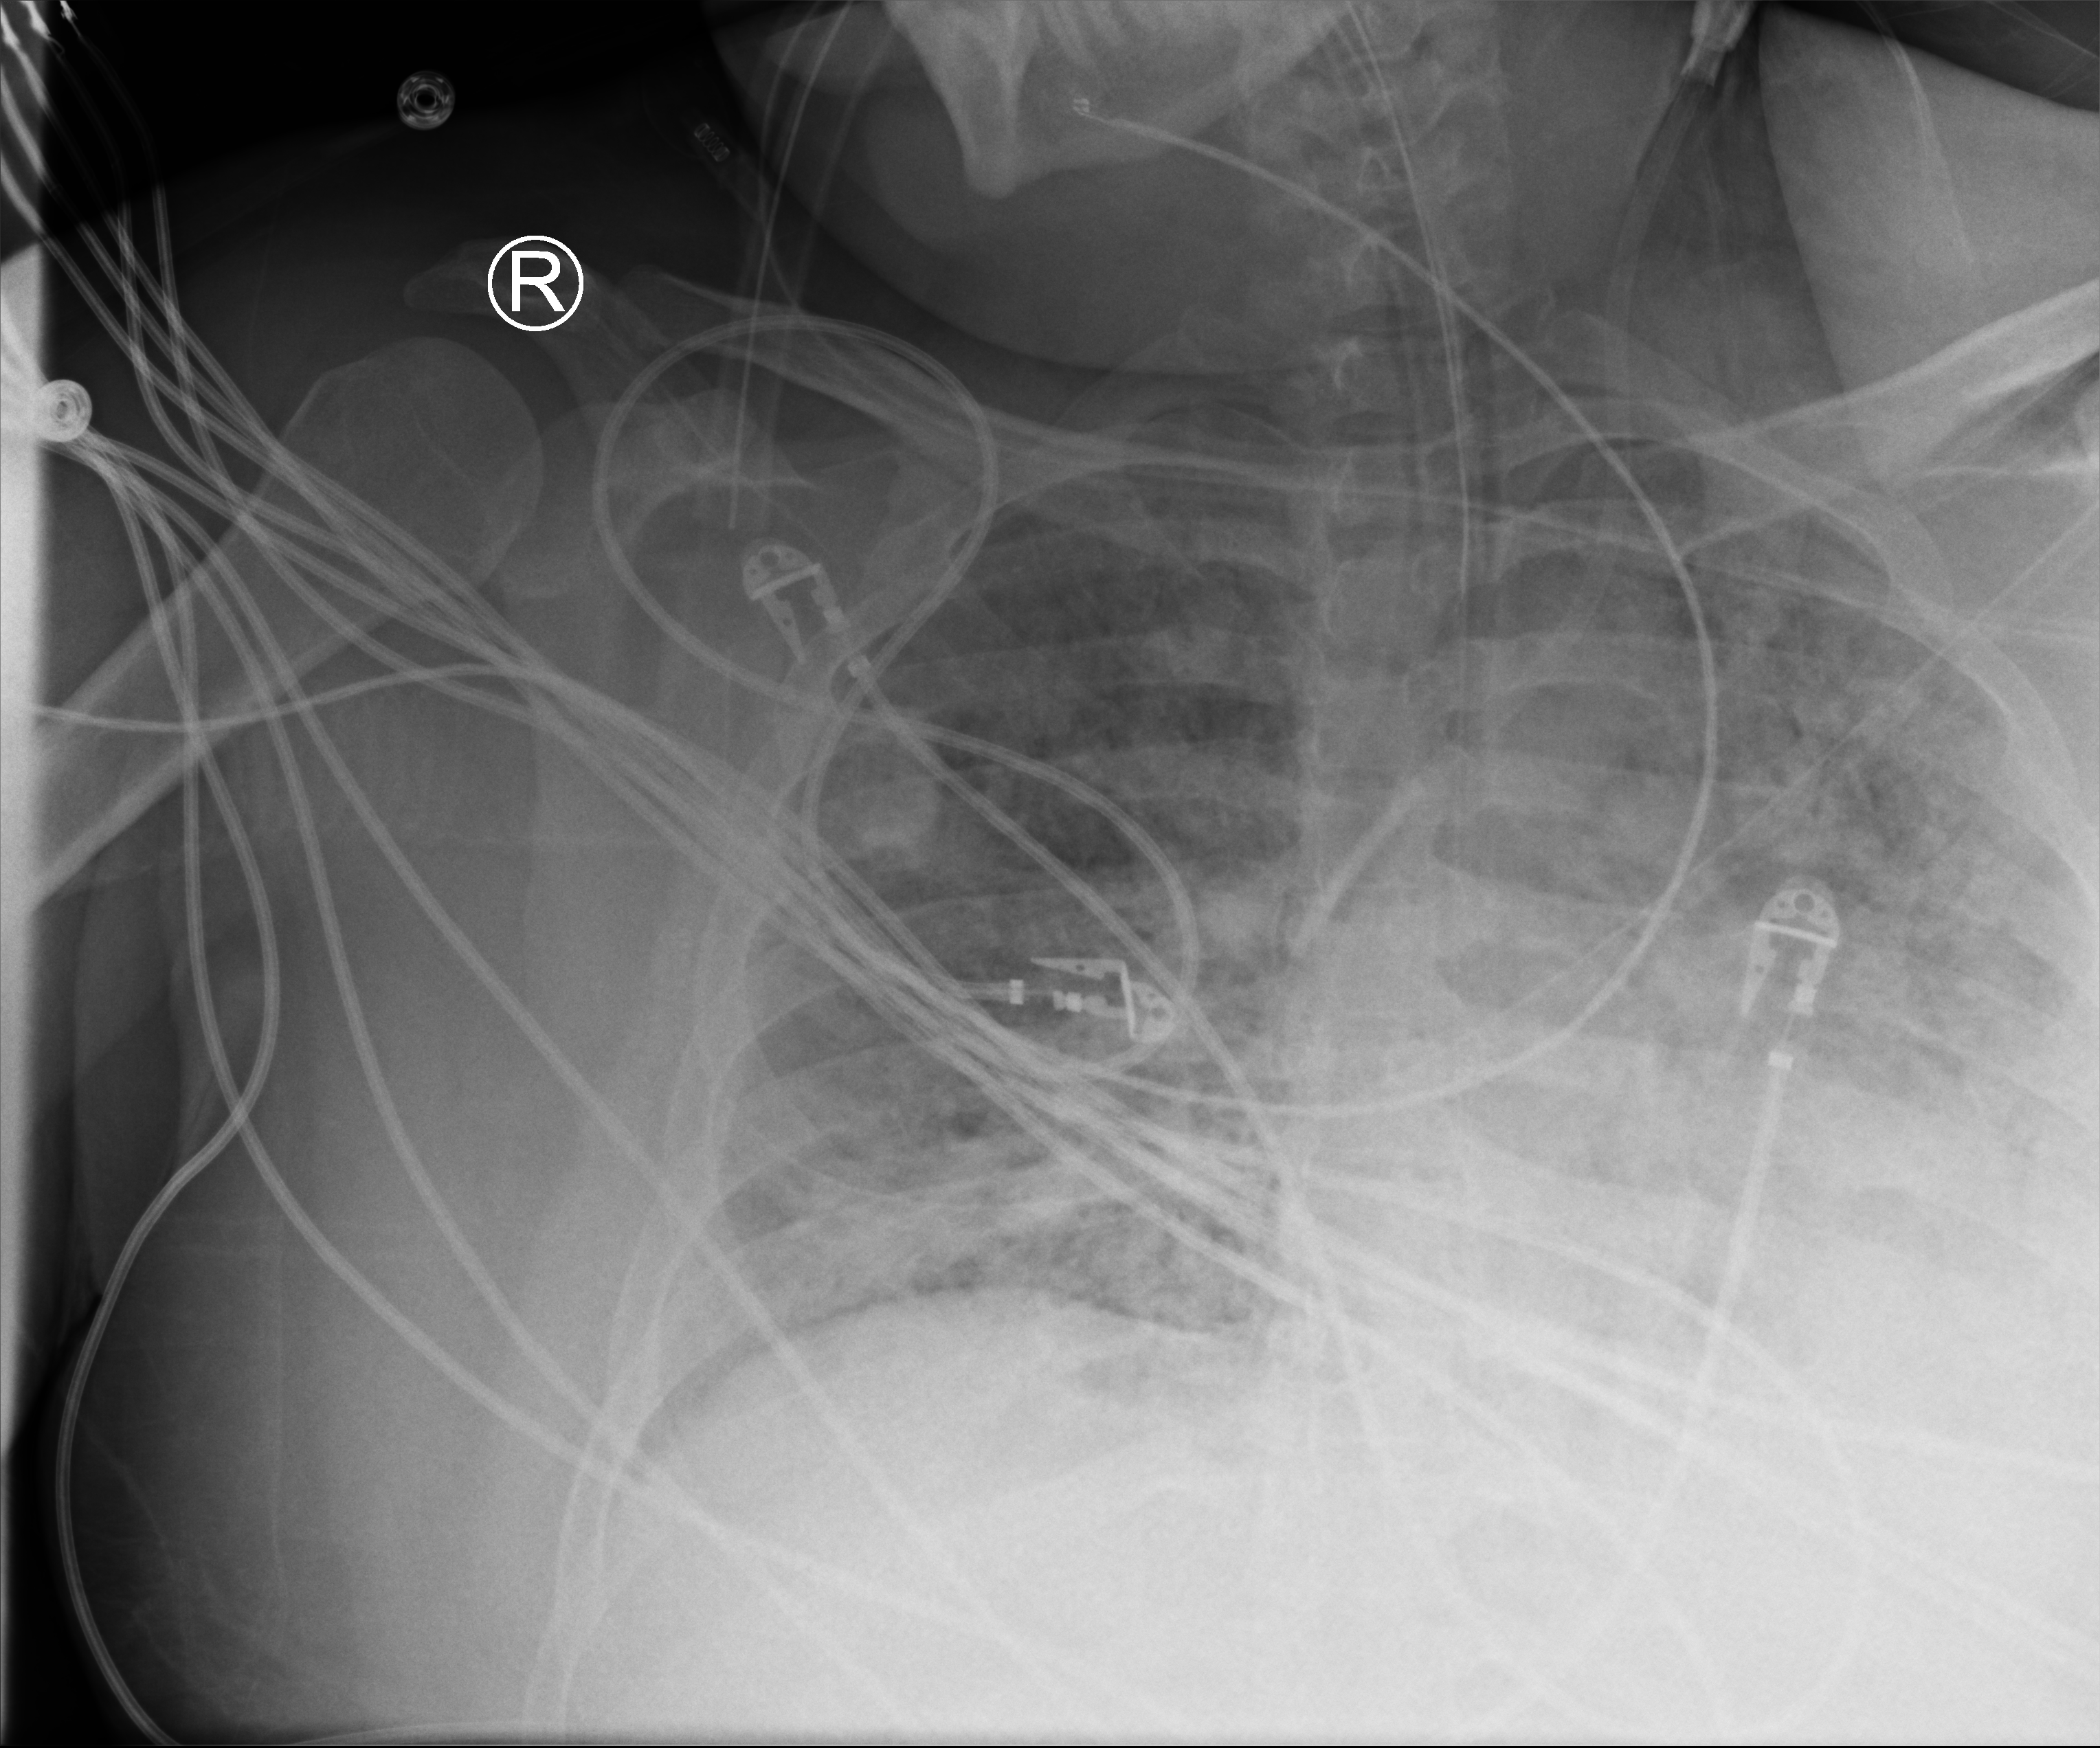
Chest X-ray (portable); anteroposterior (AP) projection. Patient hospitalised with COVID-19, aged 18–59 years.
Admission-level facts for this patient (not findings on this image; timing relative to this image not recorded):
- admitted to intensive care during this hospital stay: yes
- mechanically ventilated during this hospital stay: yes